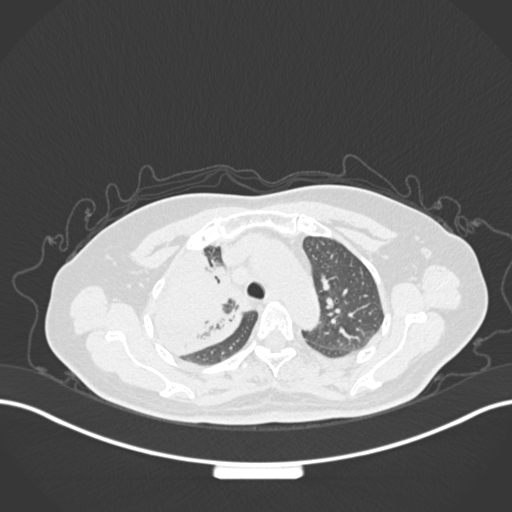
Chest CT, one axial slice; slice 118 of 177 in the series (ordered by position); reconstruction kernel B30f; 120 kVp; lung window (W 1500 / L -600 HU); 1 mm slice thickness; 512 × 512 image matrix. Patient: female, 60 years. Case-level facts recorded for this patient, not image findings: clinical TNM (as recorded): T3 N1 M1.
Outlined on this slice (bounding box drawn by a radiologist):
- lung tumour (recorded histology: adenocarcinoma): bounding box (x1, y1, x2, y2) in pixels: (145, 247, 248, 357)